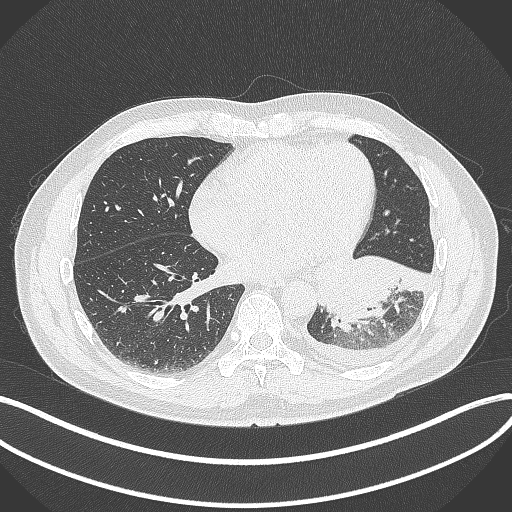
Chest CT, one axial slice; position 133 of 342 along the scan axis; reconstruction kernel B70f; lung window (W 1500 / L -600 HU); 1 mm slice thickness; 512 × 512 image matrix. Male patient, age 58 years. Case-level facts recorded for this patient, not image findings: clinical TNM (as recorded): T3 N1 M1b; histopathological grade: G3.
Outlined on this slice (rectangle marked by the reading radiologist):
- lung tumour (recorded histology: small cell carcinoma): bounding box <315,252,430,332> (left, top, right, bottom; pixels)